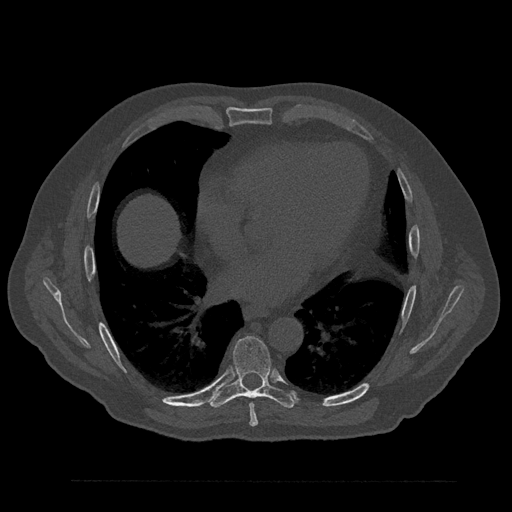
CT including the spine, one axial slice; position 467 of 797 along the scan axis; 120 kVp; bone window (W 1800 / L 400 HU); 0.5 mm slice thickness; 512 × 512 image matrix, field of view 430 × 430 mm. Patient: male, 61 years. From the clinical record (not read from this slice): primary cancer: prostate.
Outlined on this slice (semi-automatic segmentation, software-assisted and operator-edited):
- T7 vertebra: box from (x=249, y=403) to (x=258, y=427) px
- T8 vertebra: (x=210, y=336)–(x=296, y=408)